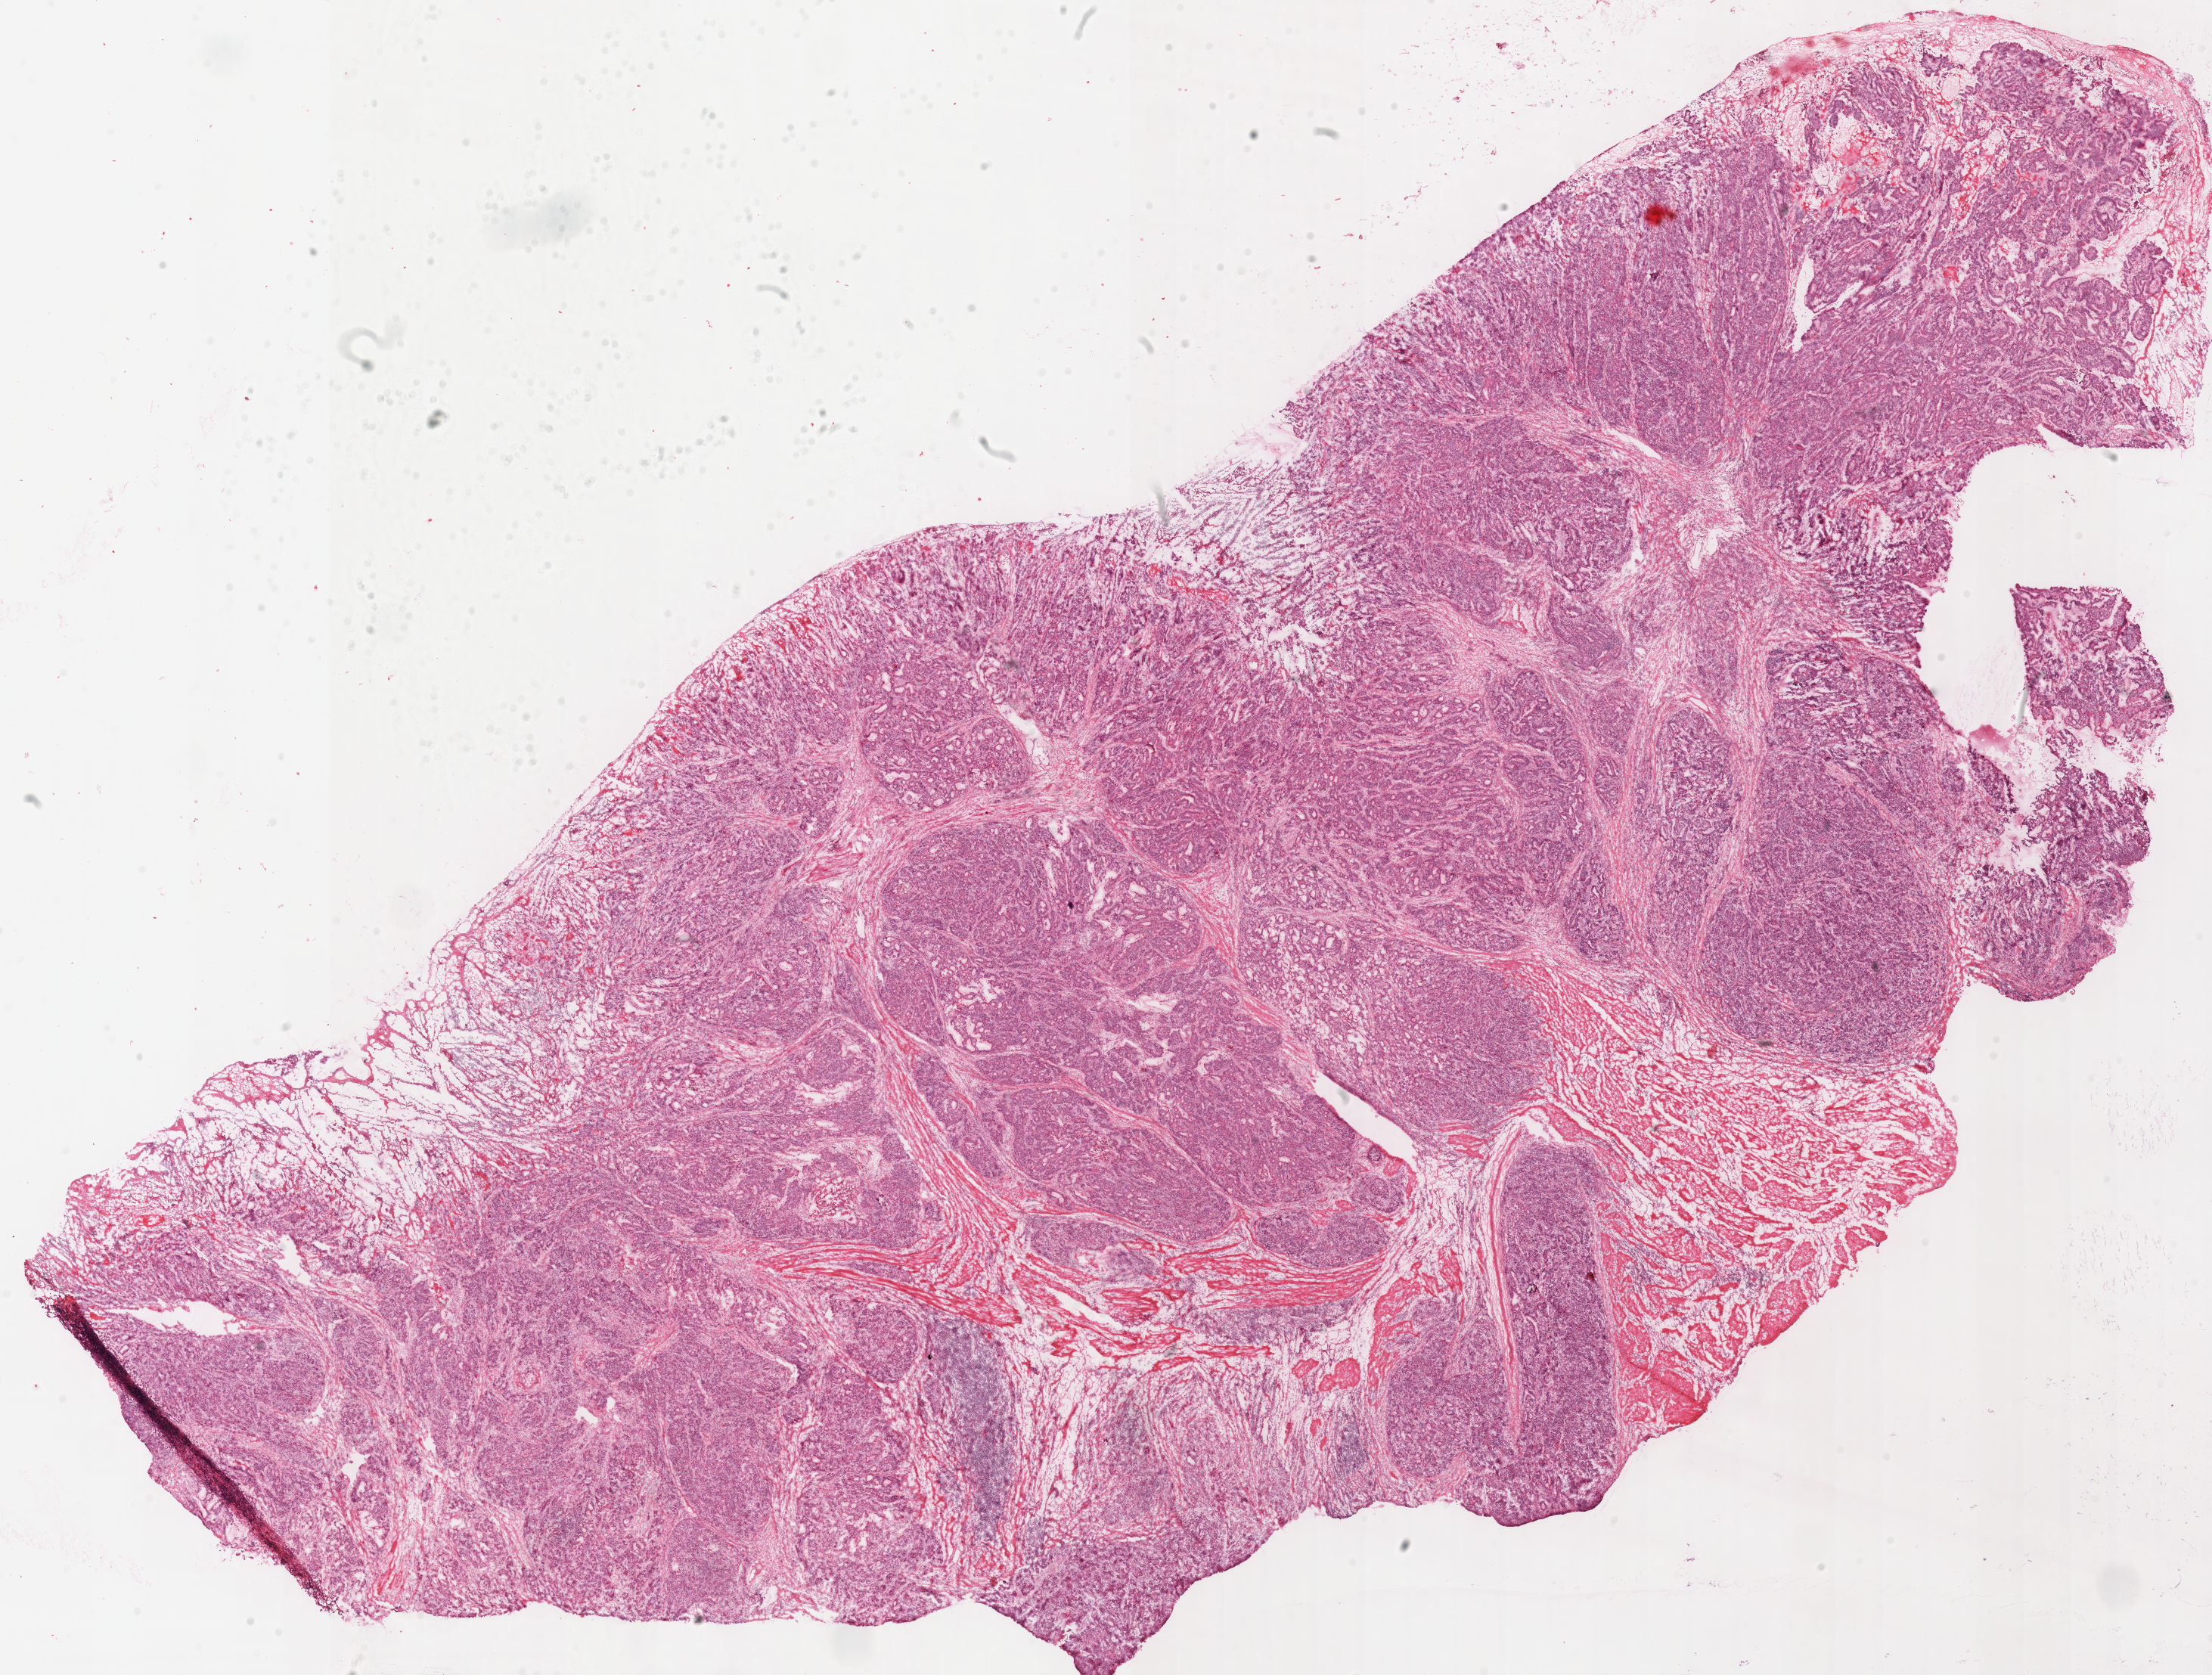
H&E-stained whole-slide image — a low-resolution overview of the entire scanned area, about 23.0 x 17.4 mm; frozen section from the top of the tissue portion; sample: primary tumour, stomach. Male patient; age at initial diagnosis 63 years. Histologic grade: G3 (poorly differentiated). Slide review estimates, as recorded: tumour cells 80%, tumour nuclei 80%, normal cells 10%, stromal cells 10%, necrosis 0%.
* histologic diagnosis: Adenocarcinoma, intestinal type (fundus of stomach)
* TNM: T4b N3a M0
* AJCC pathologic stage: IIIC (7th edition)